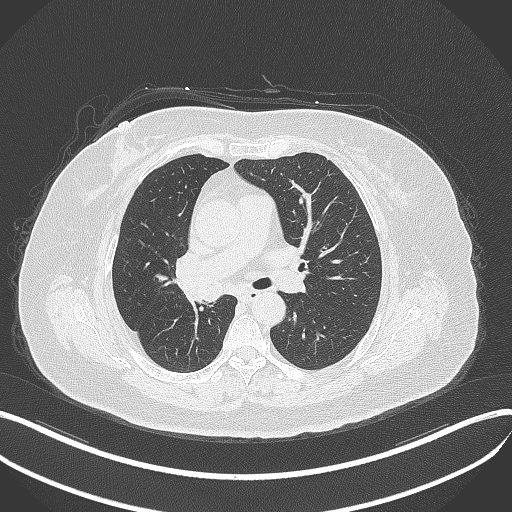
Chest CT, one axial slice; position 212 of 376 along the scan axis; reconstruction kernel B70f; lung window (W 1500 / L -600 HU); 512 × 512 image matrix. Patient: female, 60 years. Case-level facts recorded for this patient, not image findings: clinical TNM (as recorded): T1c N0 M0; histopathological grade: G1-G2.
Structures marked on this image (bounding box drawn by a radiologist):
- lung tumour (recorded histology: squamous cell carcinoma): bounding box <183,276,225,306> (left, top, right, bottom; pixels)